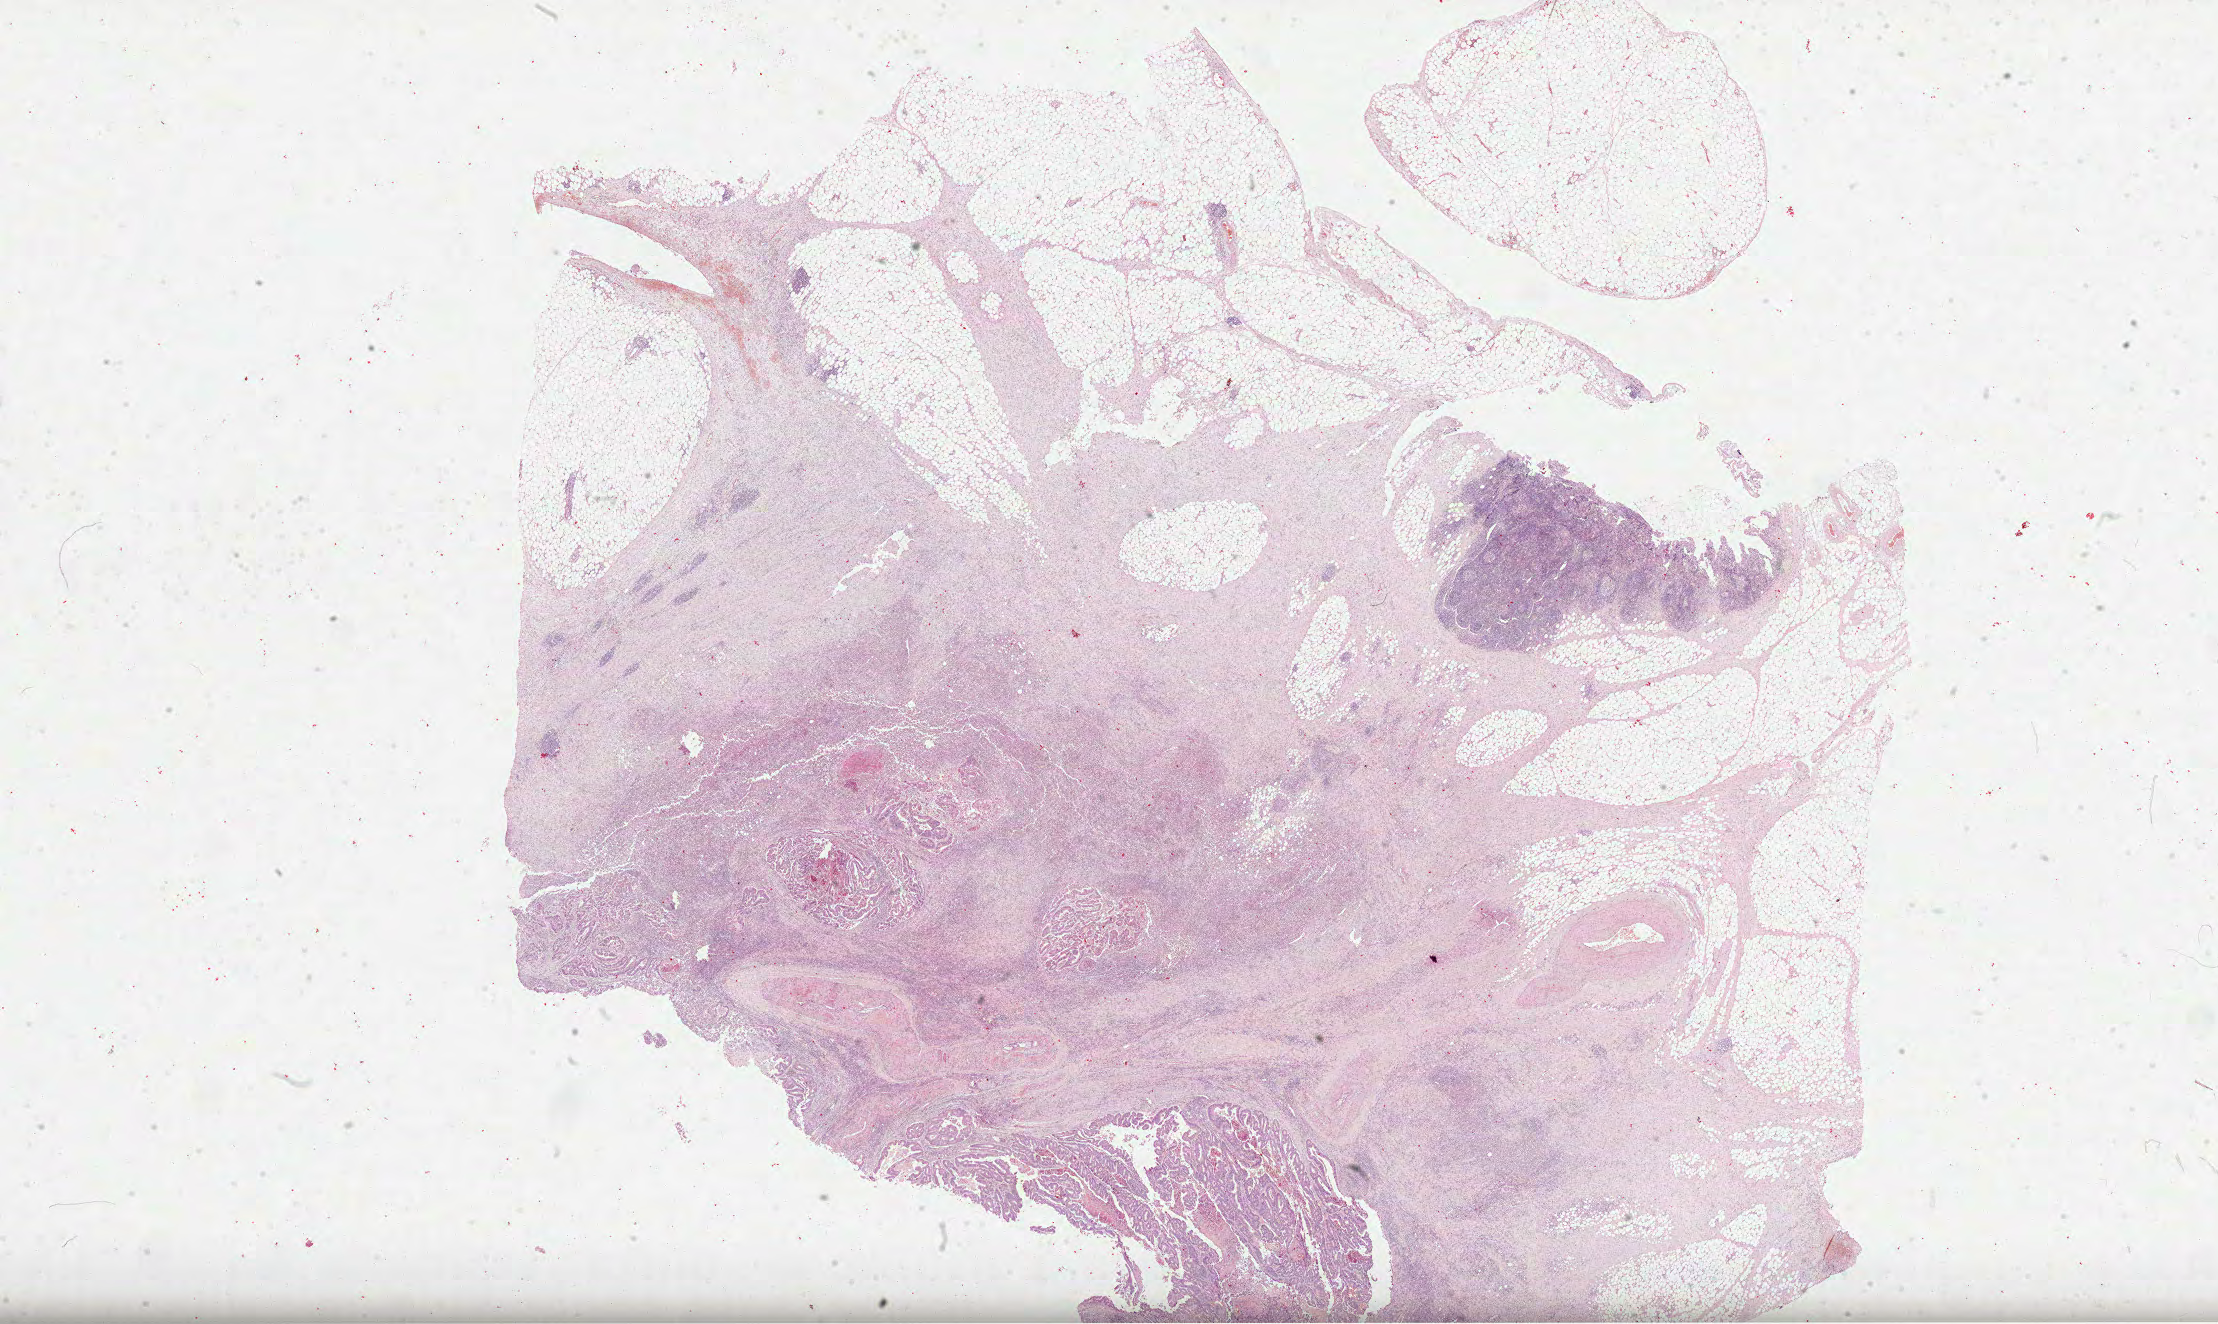
Digitized Hematoxylin and eosin (H&E) stained tissue section (whole slide), shown as a low-resolution overview of the whole scanned area (about 35.8 x 21.4 mm, slide scanned at 40x); FFPE section; primary tumour sample from the colon. Male, age 61 years at initial diagnosis.
AJCC pathologic stage: IIA. Pathologic diagnosis: Adenocarcinoma, NOS (sigmoid colon). Lymph nodes positive (case pathology): 0 of 10 examined. TNM: T3 N0 M0.